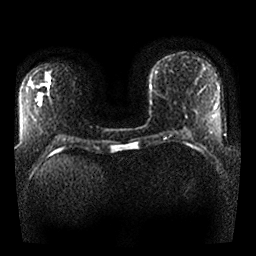
Breast MRI, one axial slice; slice 12 of 25 in the series (ordered by position); diffusion-weighted series; image 2 of 4 stored at this slice position (different b-values; order by instance number); 1.5 T; 256 × 256 image matrix, field of view 330 × 330 mm. Female patient.
Structures marked on this image (outlined manually by an expert reader):
- tumour on diffusion-weighted imaging: box from (x=45, y=75) to (x=51, y=82) px